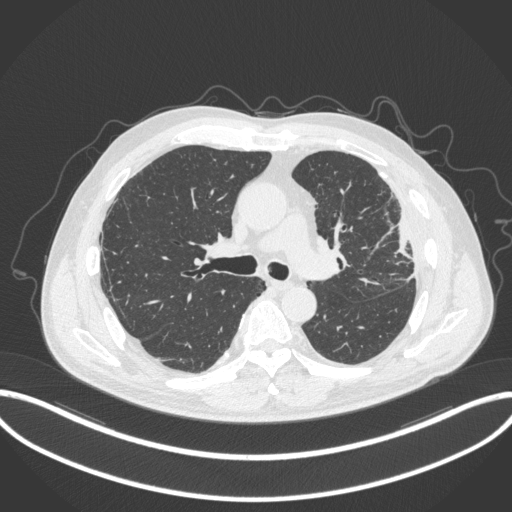
Chest CT, one axial slice. Position 214 of 382 along the scan axis. Lung window (W 1500 / L -600 HU). 1 mm slice thickness. 512 × 512 image matrix, field of view 415 × 415 mm. Patient: male, 64 years. From the clinical record (not read from this slice): clinical TNM (as recorded): T4 N1 M0; histopathological grade: G3.
Annotated regions visible in this slice (bounding box drawn by a radiologist):
- lung tumour (recorded histology: adenocarcinoma): bounding box [x1, y1, x2, y2] px = [383, 210, 419, 260]